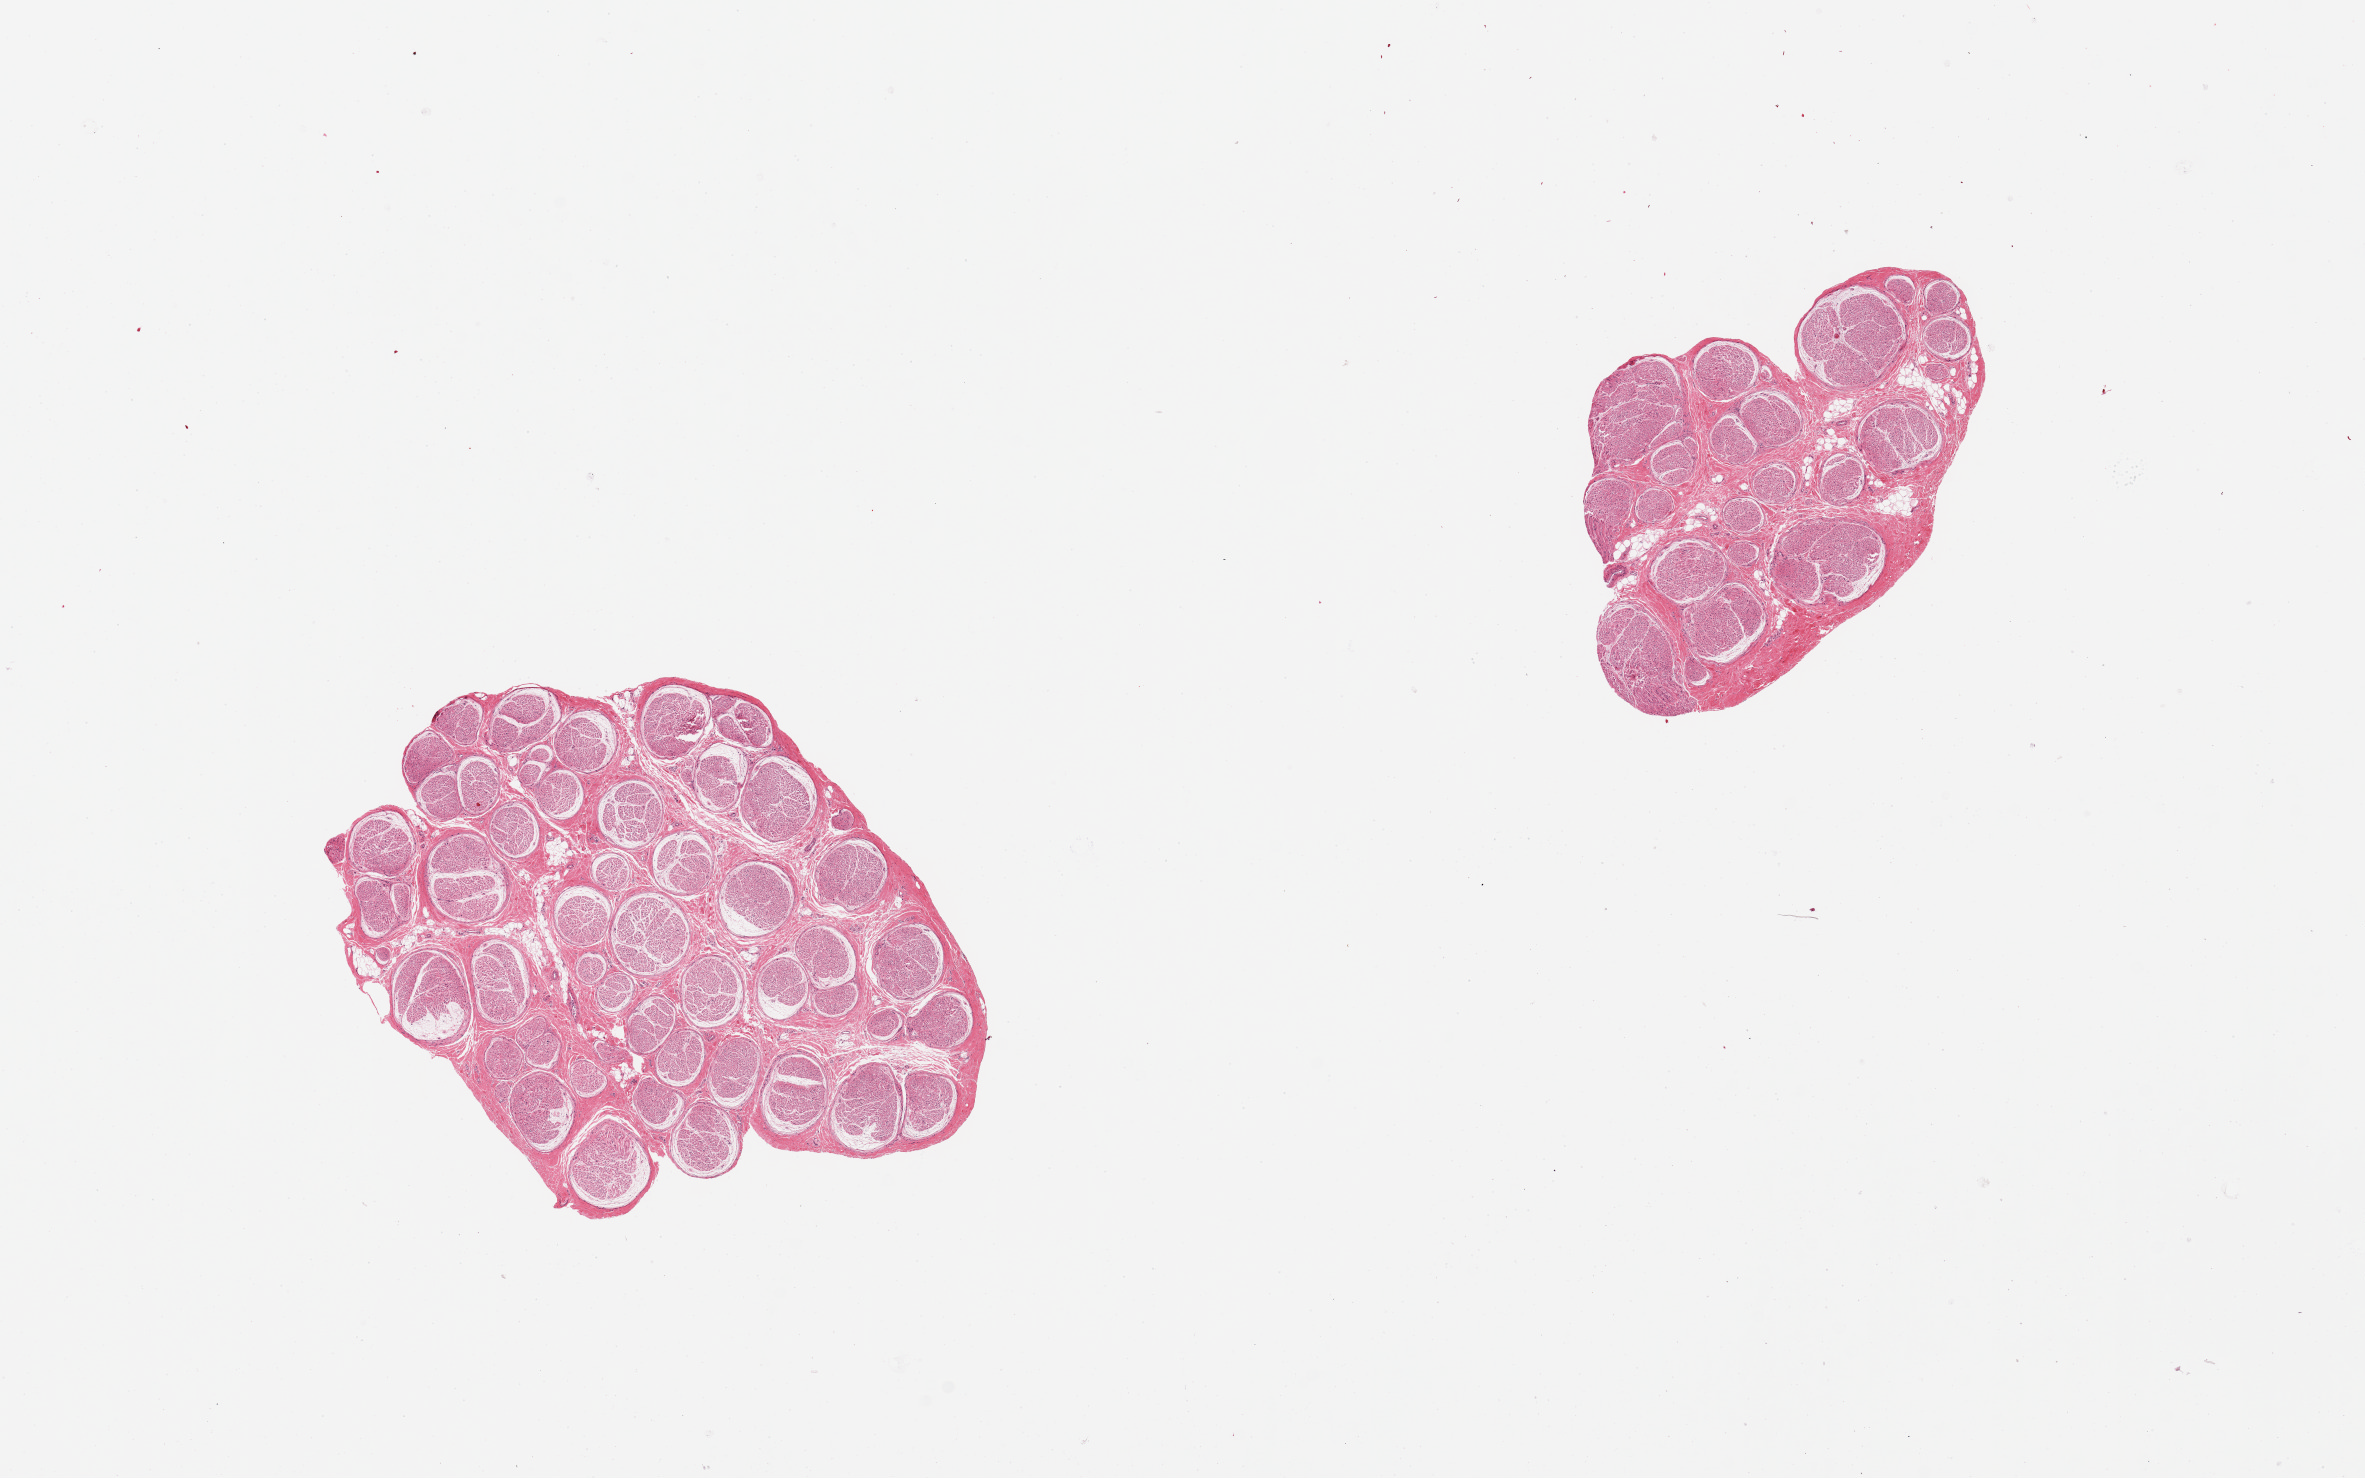
Hematoxylin and eosin (H&E) whole-slide image — shown as a low-resolution overview of the whole scanned area (about 18.7 x 11.7 mm); PAXgene-fixed paraffin-embedded (PFPE) section; section of tibial nerve (target tissue); donor tissue sample. Donor sex: male.
Review note (as recorded): 2 pieces, good clean specimens.